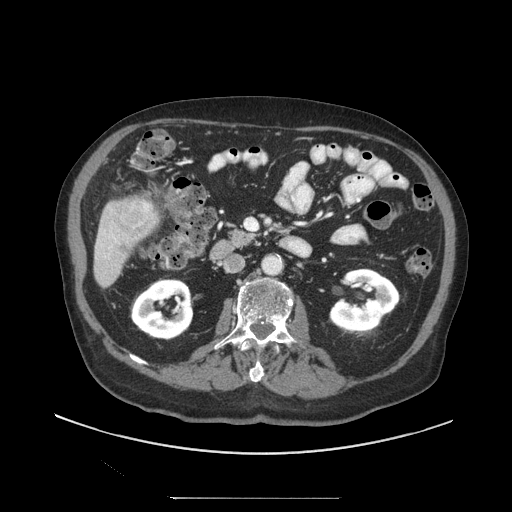
Contrast-enhanced abdominal CT (liver protocol), one axial slice. 140 kVp. Soft-tissue window (W 400 / L 40 HU). 2.5 mm slice thickness. 512 × 512 image matrix, field of view 450 × 450 mm. From the clinical record (not read from this slice): diagnosis: hepatocellular carcinoma (patient treated with transarterial chemoembolisation; whether this scan precedes or follows treatment is not stated here); TNM stage (as recorded): Stage-IIIC; Child-Pugh class: A; tumour nodularity: uninodular.
Outlined on this slice (semi-automatic segmentation, software-assisted and operator-edited):
- liver parenchyma outside the tumour (the mass and vessels are separate outlines, so this box may not span the whole liver): bounding box <94,196,158,288> (left, top, right, bottom; pixels)
- liver vessels: <113,203,149,237>